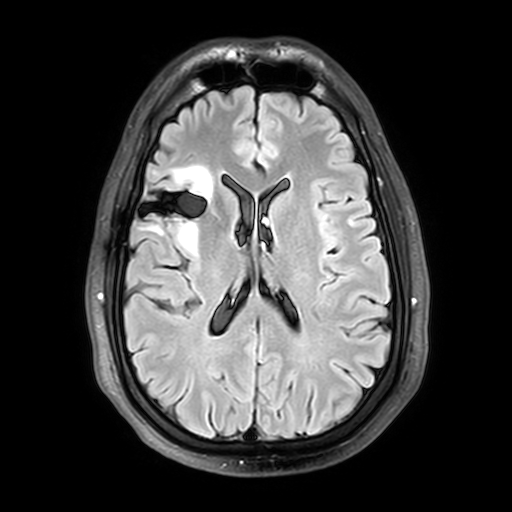
Brain MRI from a brain-tumour surgery series, one axial slice. Slice 18 of 42 in the series (ordered by position). T2 FLAIR. 512 × 512 image matrix, field of view 240 × 240 mm. Case-level facts recorded for this patient, not image findings: histopathology: Astrocytoma; WHO grade: 2; IDH mutation: yes.
Structures marked on this image (manually delineated by an expert):
- tumour: bounding box <137,166,223,256> (left, top, right, bottom; pixels)